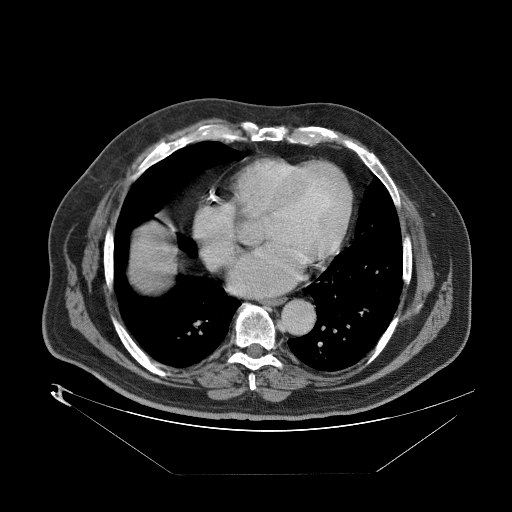
Contrast-enhanced abdominal CT (liver protocol), one axial slice; slice 85 of 89 in the series (ordered by position); reconstruction kernel STANDARD; 140 kVp; one of 2 acquisitions stored at this slice position; soft-tissue window (W 400 / L 40 HU); 512 × 512 image matrix, field of view 480 × 480 mm. From the clinical record (not read from this slice): diagnosis: hepatocellular carcinoma (patient treated with transarterial chemoembolisation; whether this scan precedes or follows treatment is not stated here); TNM stage (as recorded): Stage-II; Child-Pugh class: B; tumour differentiation: moderately differentiated; tumour nodularity: multinodular.
Structures marked on this image (semi-automatic segmentation, software-assisted and operator-edited):
- abdominal aorta: box from (x=279, y=299) to (x=313, y=334) px